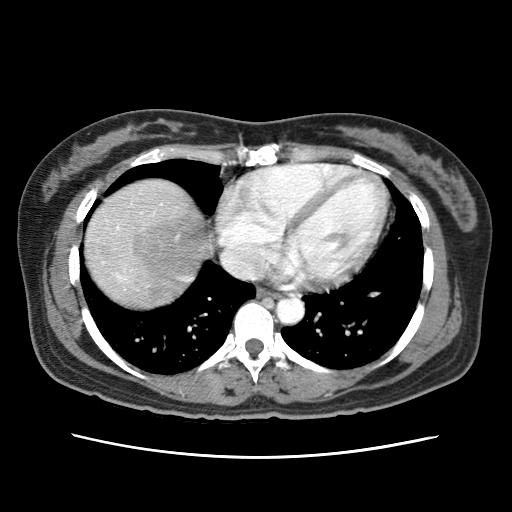
Contrast-enhanced abdominal CT (liver protocol), one axial slice. Slice 65 of 79 in the series (ordered by position). Reconstruction kernel STANDARD. 120 kVp. Soft-tissue window (W 400 / L 40 HU). 2.5 mm slice thickness. 512 × 512 image matrix, field of view 340 × 340 mm. From the clinical record (not read from this slice): diagnosis: hepatocellular carcinoma (patient treated with transarterial chemoembolisation; whether this scan precedes or follows treatment is not stated here); TNM stage (as recorded): Stage-I; Child-Pugh class: A; tumour nodularity: uninodular.
Outlined on this slice (semi-automatically segmented with operator editing):
- abdominal aorta: bounding box [x1, y1, x2, y2] px = [276, 297, 303, 325]
- liver parenchyma outside the tumour (the mass and vessels are separate outlines, so this box may not span the whole liver): [84, 180, 200, 306]
- liver vessels: [117, 227, 121, 278]